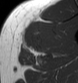
MRI of an extremity soft-tissue mass, one axial slice; slice 34 of 43 in the series (ordered by position); MR volume resampled by the dataset authors to the PET/CT grid (not the native acquisition matrix); 78 × 83 image matrix. Male patient. From the clinical record (not read from this slice): histological type: pleiomorphic leiomyosarcoma; grade: high; site of the primary tumour: left thigh.
Outlined on this slice (expert contour drawn on MRI and transferred to this co-registered scan by the dataset authors):
- gross tumour volume including surrounding oedema: box from (x=20, y=28) to (x=42, y=54) px